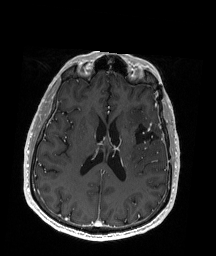
Brain MRI from a brain-tumour surgery series, one axial slice; position 83 of 192 along the scan axis; T1-weighted post-contrast; 1 mm slice thickness; 216 × 256 image matrix, field of view 211 × 250 mm. From the clinical record (not read from this slice): histopathology: Oligodendroglioma; WHO grade: 2; IDH mutation: yes; tumour location: Left Insular.
Outlined on this slice (manually delineated by an expert):
- previous resection cavity: bounding box <136,121,160,148> (left, top, right, bottom; pixels)